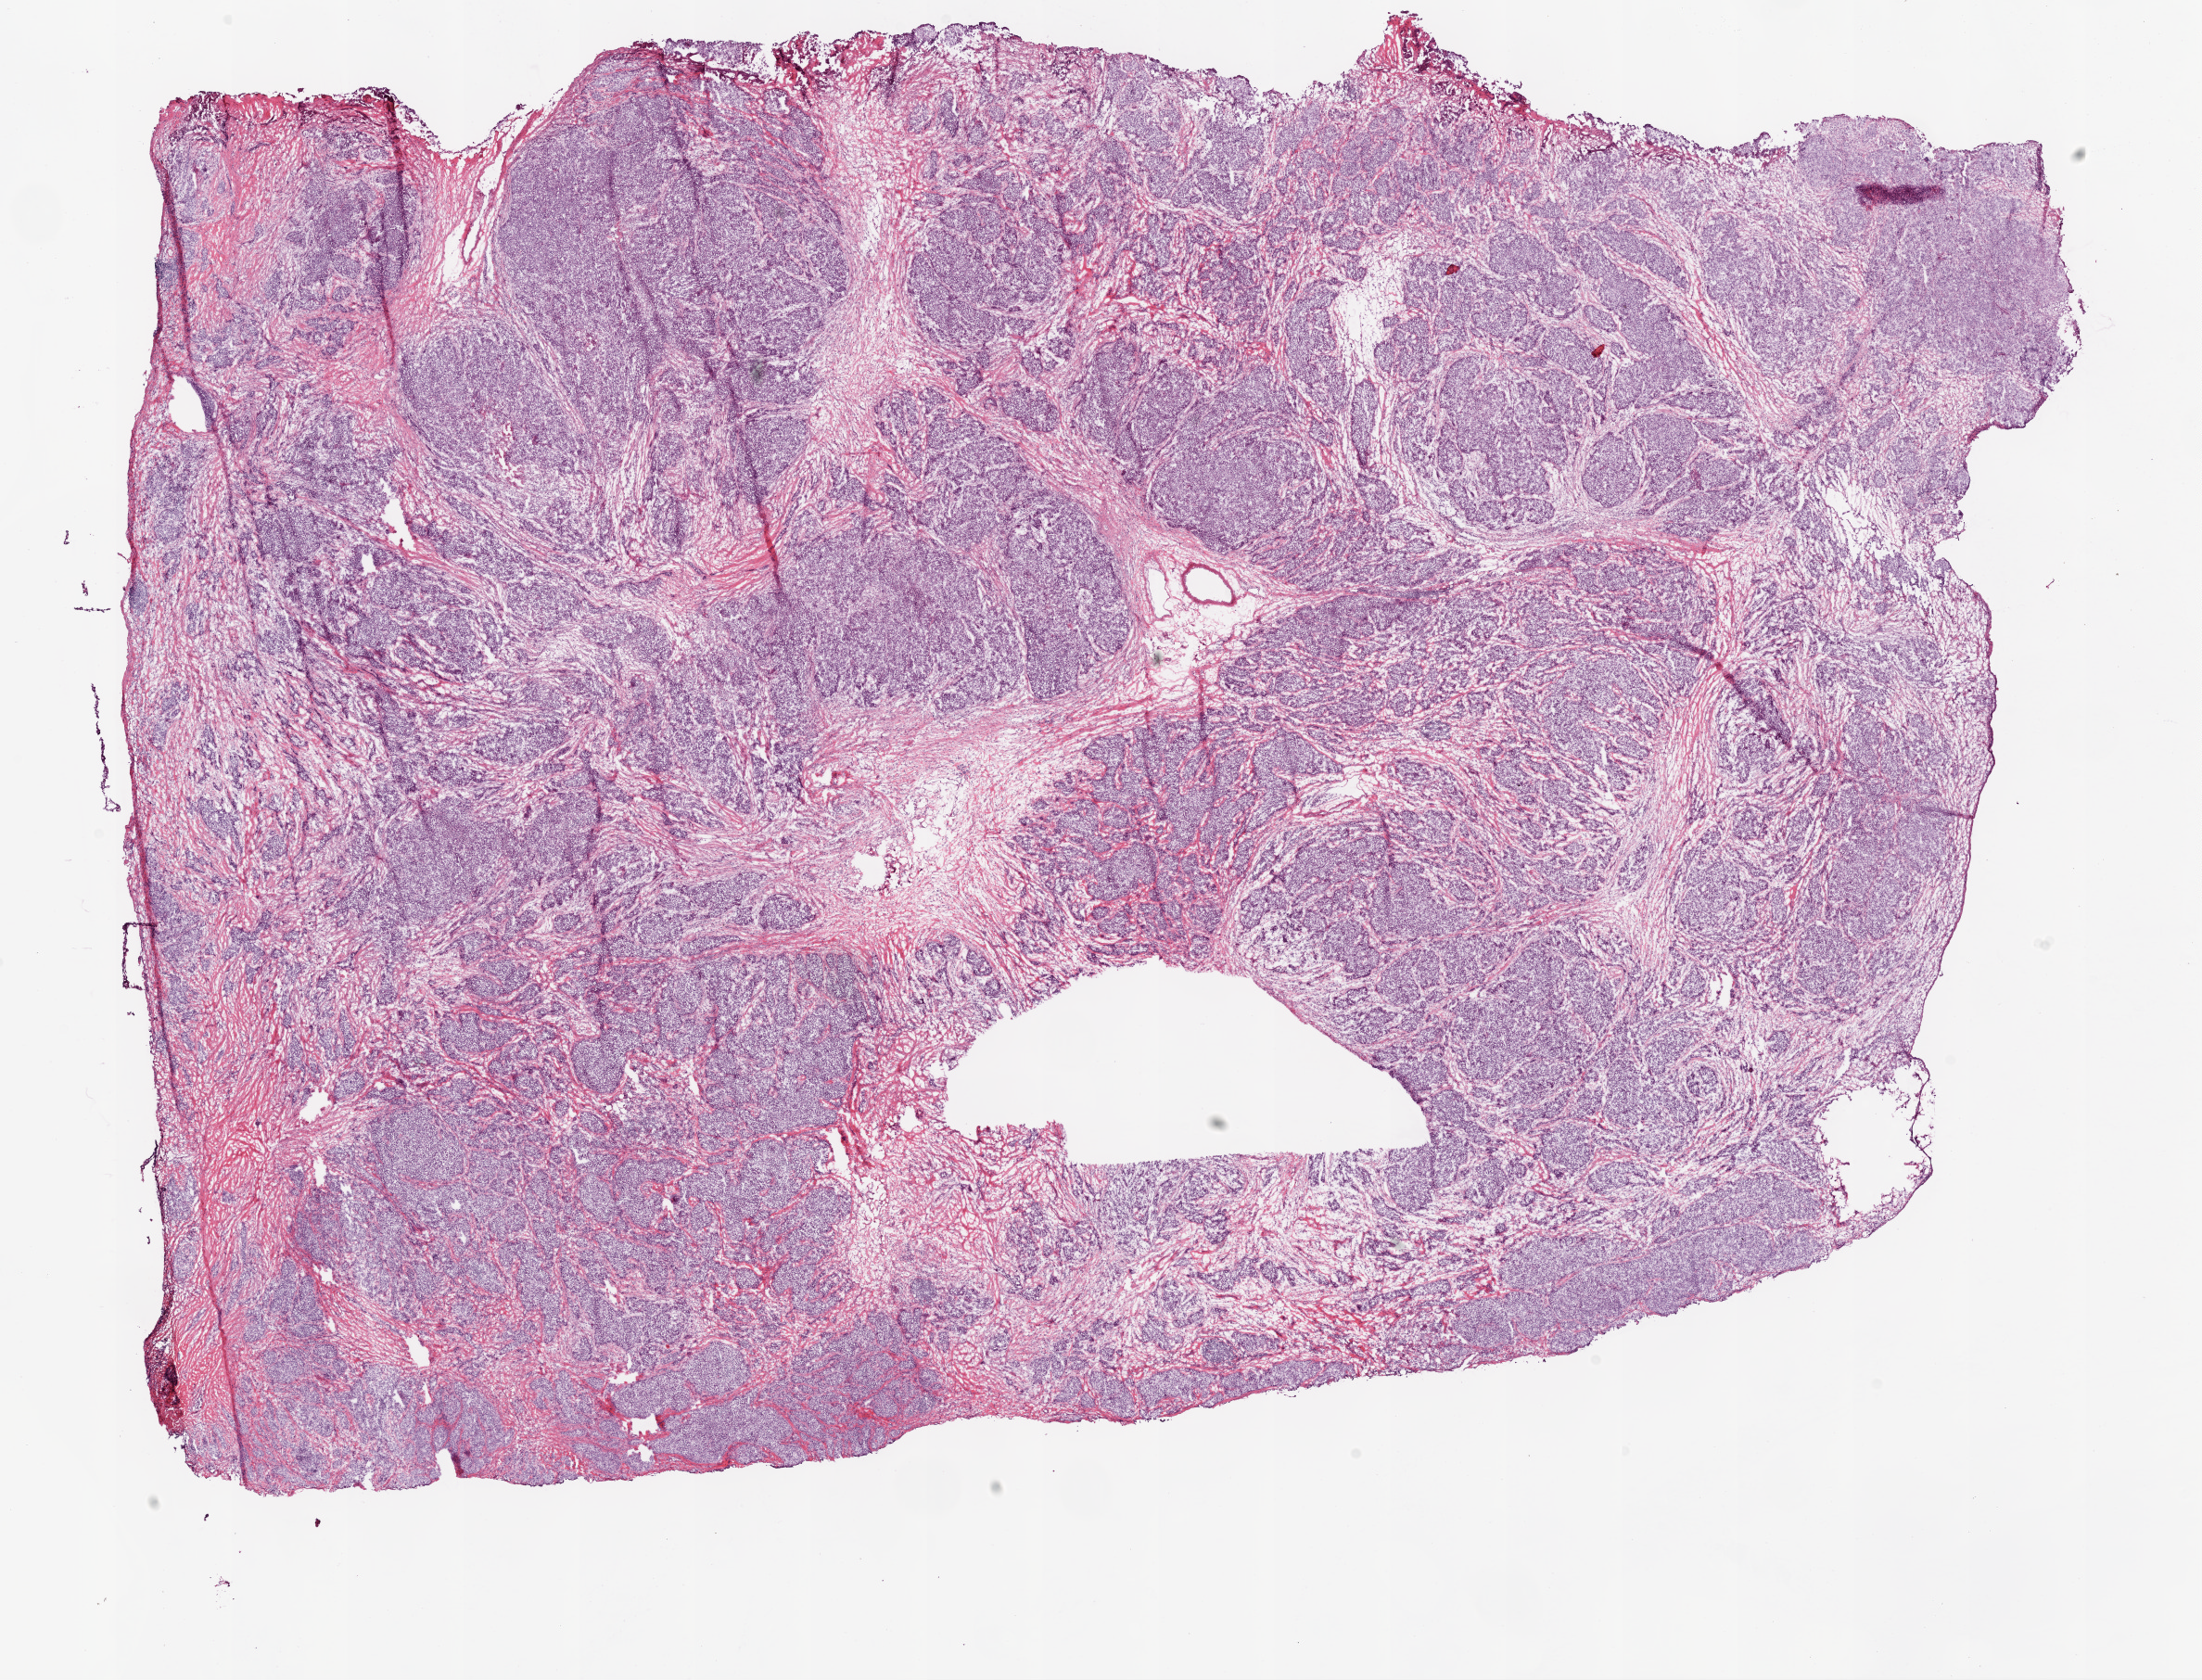
H&E-stained whole-slide image, whole scanned area (about 19.1 x 14.5 mm, from a 20x scan) shown as a low-resolution overview; frozen section from the bottom of the tissue portion; ovary, primary tumour sample. Female patient; age at initial diagnosis 60 years. Histologic grade: G3 (poorly differentiated). Composition of this section per pathologist review: tumour cells 80%, tumour nuclei 90%, normal cells 0%, stromal cells 15%, necrosis 5%.
* FIGO stage: IIIC
* diagnosis: Serous cystadenocarcinoma, NOS